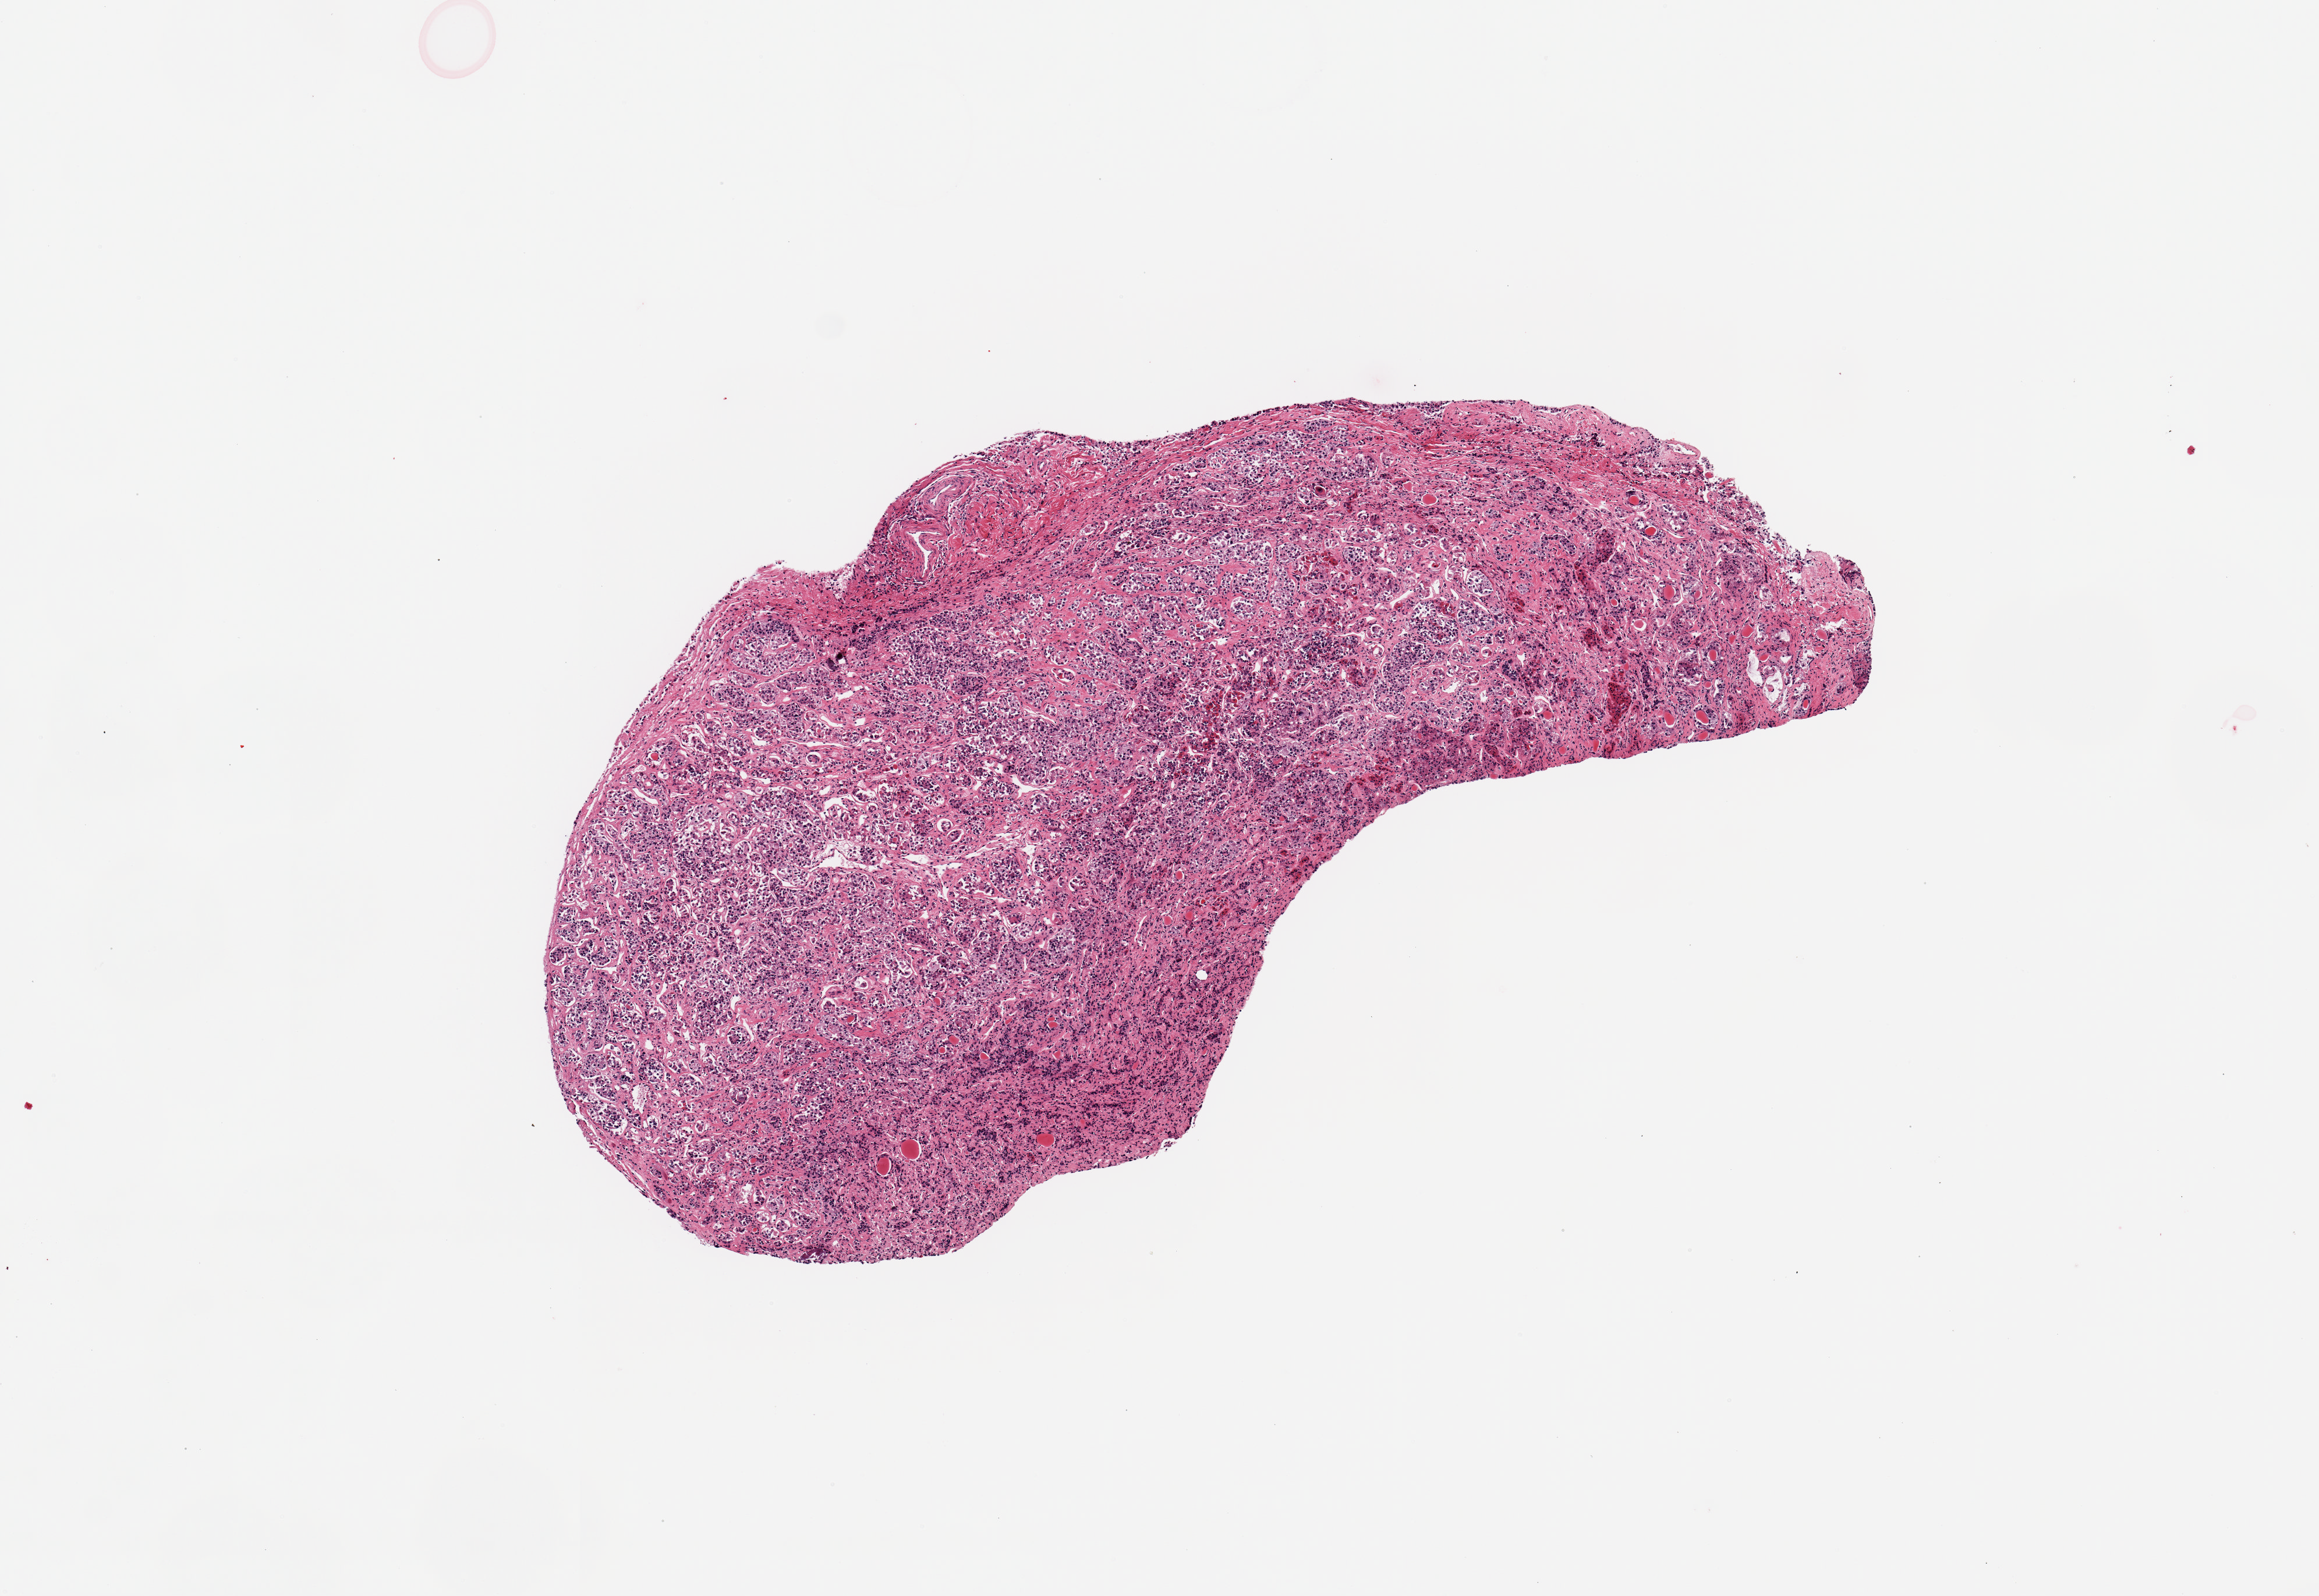
Digitized haematoxylin and eosin-stained section — shown as a low-resolution overview of the whole scanned area (about 7.9 x 5.4 mm, slide scanned at 20x). PAXgene-fixed paraffin-embedded (PFPE) section. Section of pituitary (target tissue). Donor tissue sample. Female donor.
• review note (as recorded): 1 piece; mostly anterior lobe; no neurohypophysis in this cut